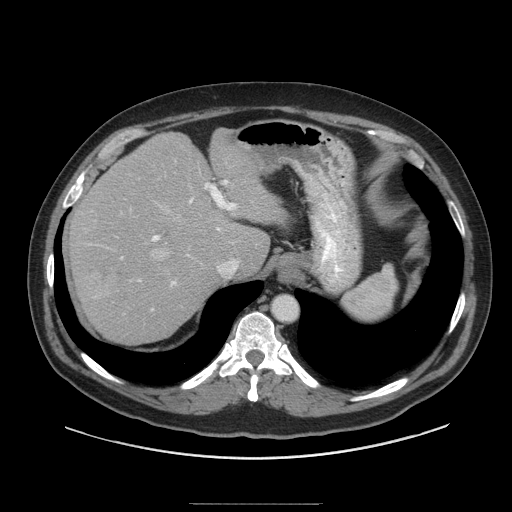
Contrast-enhanced abdominal CT (liver protocol), one axial slice; slice 71 of 91 in the series (ordered by position); reconstruction kernel STANDARD; 140 kVp; soft-tissue window (W 400 / L 40 HU); 2.5 mm slice thickness; 512 × 512 image matrix, field of view 440 × 440 mm. From the clinical record (not read from this slice): diagnosis: hepatocellular carcinoma (patient treated with transarterial chemoembolisation; whether this scan precedes or follows treatment is not stated here); TNM stage (as recorded): Stage-I; Child-Pugh class: A; tumour differentiation: well differentiated.
Structures marked on this image (semi-automatically segmented with operator editing):
- abdominal aorta: bounding box (x1, y1, x2, y2) in pixels: (273, 297, 297, 320)
- liver parenchyma outside the tumour (the mass and vessels are separate outlines, so this box may not span the whole liver): (68, 128, 284, 344)
- mass: (91, 256, 128, 290)
- liver vessels: (90, 180, 237, 286)